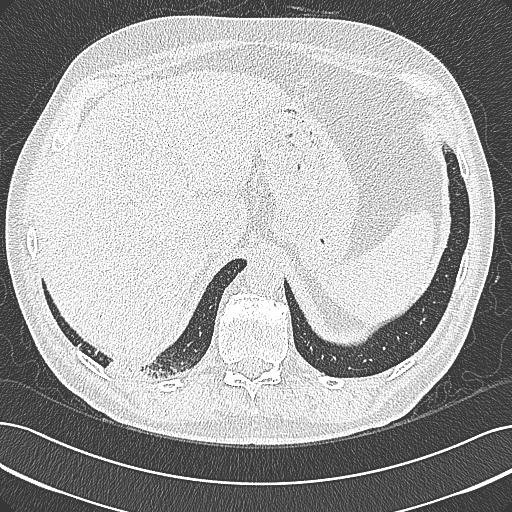
Axial slice from a low-dose chest CT screening exam; first (baseline) screen; lung window (W 1500 / L -600 HU); 1 mm slice thickness; lung (sharp) reconstruction kernel (B80f). Male participant, aged 68 years at enrolment. Former smoker at enrolment.
Lesion marked by an expert reader, bounding box (x1, y1, x2, y2) in pixels: (93, 335, 198, 395). Screening reader's record for this exam: no non-calcified nodule ≥4 mm recorded. Official screen result: negative screen, significant abnormalities not suspicious for lung cancer. Later outcome: lung cancer diagnosed 154 days after this screen — mucinous adenocarcinoma, right lower lobe, well differentiated (G1), stage IB (AJCC 6th edition), 50 mm at pathology.